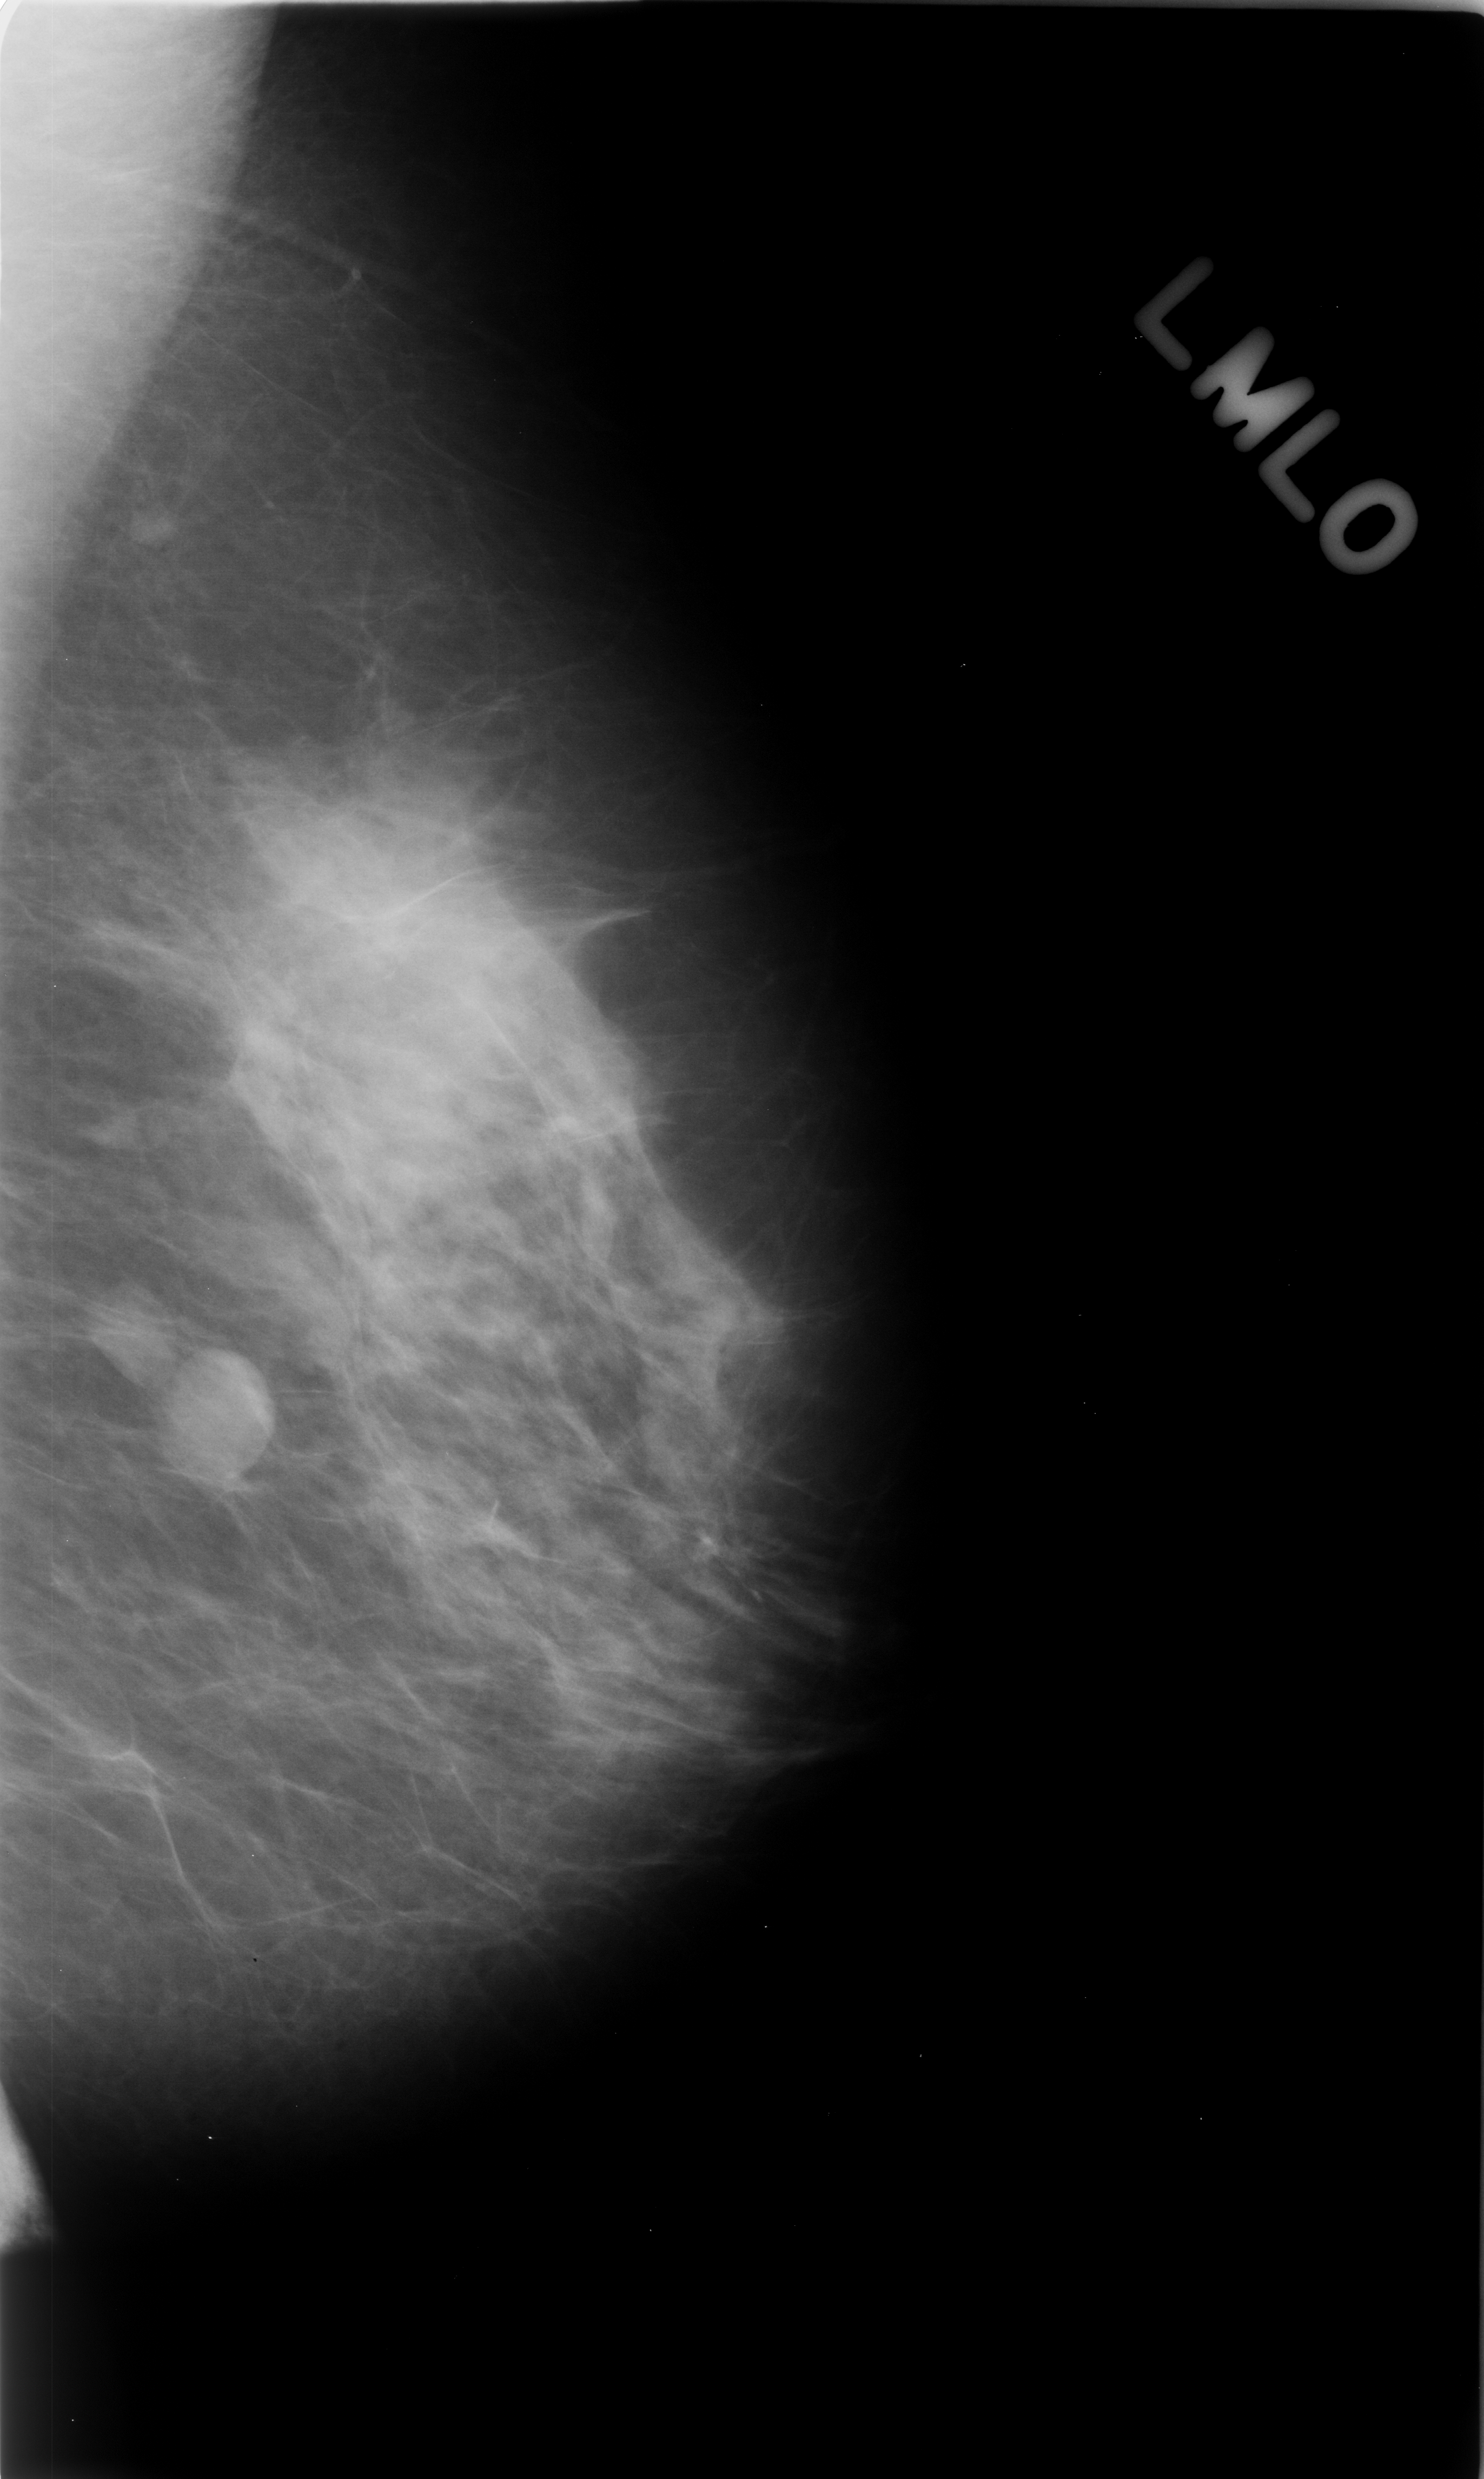
Digitized screen-film mammogram; left breast; mediolateral oblique (MLO) view; BI-RADS breast density category 2 (scale 1–4); 1484 × 2479 image matrix.
Marked abnormalities (boxes around the expert regions of interest):
- Finding 1 of 2: mass, shape oval, margins circumscribed; BI-RADS assessment category 3; pathology result (as recorded, not read from the image): benign: bounding box (x1, y1, x2, y2) in pixels: (67, 1274, 195, 1387)
- Finding 2 of 2: mass, shape oval, margins circumscribed; BI-RADS assessment category 3; subtlety rating 5 on a 1 (subtle) to 5 (obvious) scale; pathology result (as recorded, not read from the image): benign: (158, 1348, 284, 1503)